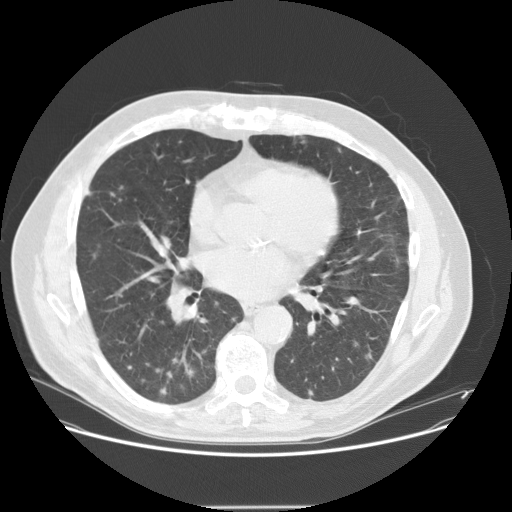
Low-dose screening chest CT, one axial slice. Position 69 of 143 along the scan axis. Reconstruction kernel STANDARD. 120 kVp. Lung window (W 1500 / L -600 HU). 2.5 mm slice thickness. 512 × 512 image matrix, field of view 400 × 400 mm.
Annotated regions visible in this slice (expert manual segmentation):
- lesion 7 (tumor): bounding box [x1, y1, x2, y2] px = [365, 349, 373, 360]